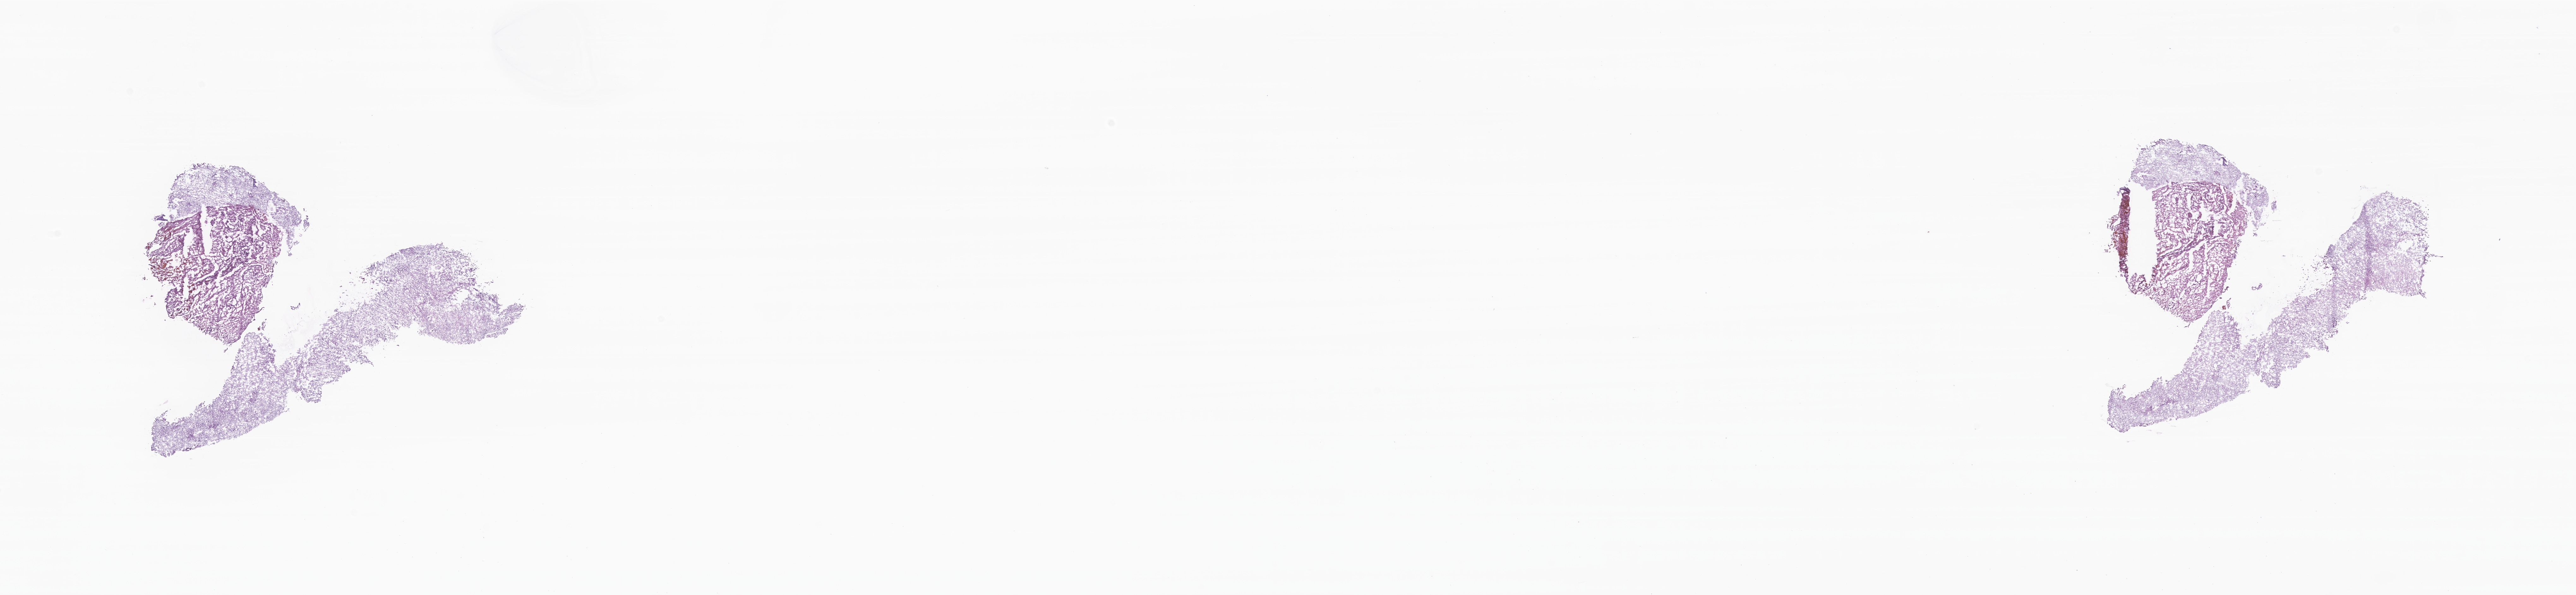
Hematoxylin and eosin (H&E) whole-slide image of tumor tissue from the brain, low-resolution overview of the scanned area, about 34.4 x 7.9 mm; frozen section (OCT-embedded). Patient: male, age 72 months (6 years).
Recorded diagnosis: Astrocytoma, NOS.